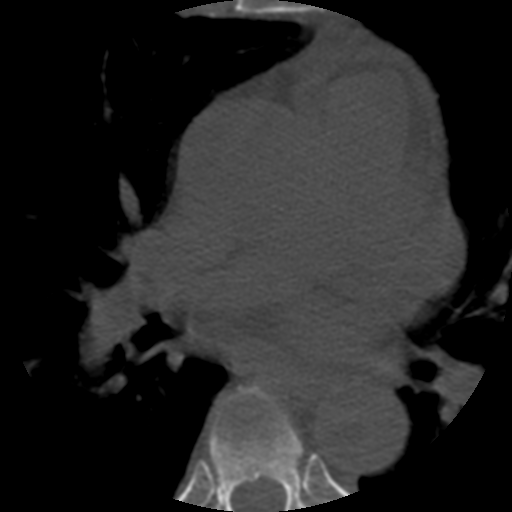
CT including the spine, one axial slice; slice 362 of 508 in the series (ordered by position); reconstruction kernel STANDARD; bone window (W 1800 / L 400 HU); 1.25 mm slice thickness; 512 × 512 image matrix. Patient age 57 years. Case-level facts recorded for this patient, not image findings: primary cancer: prostate.
Outlined on this slice (semi-automatically segmented with operator editing):
- T5 vertebra: bounding box <213,413,288,439> (left, top, right, bottom; pixels)
- T6 vertebra: <209,386,313,512>